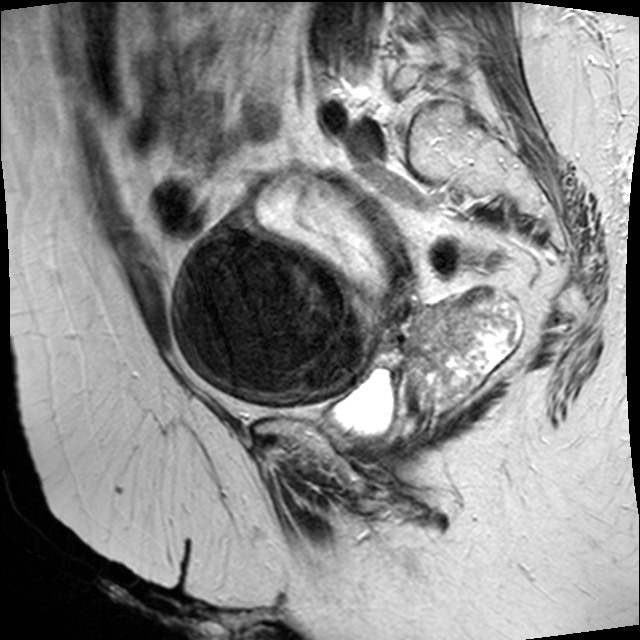
Pelvic MRI for cervical cancer, one sagittal slice. Slice 18 of 45 in the series (ordered by position). T2-weighted. 1.5 T. TE 89 ms, TR 4610 ms. 4 mm slice thickness. 640 × 640 image matrix. Patient: female, 50 years.
Structures marked on this image (expert manual segmentation):
- uterus and cervix: bounding box (x1, y1, x2, y2) in pixels: (169, 175, 522, 420)